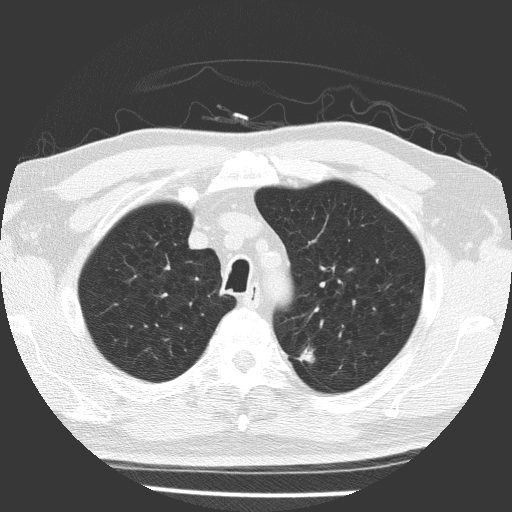
Low-dose screening chest CT, one axial slice; reconstruction kernel FC51; 120 kVp; lung window (W 1500 / L -600 HU); 512 × 512 image matrix.
Structures marked on this image (manually delineated by an expert):
- lesion 1 (tumor, upper lobe of left lung): bounding box (x1, y1, x2, y2) in pixels: (298, 346, 314, 363)